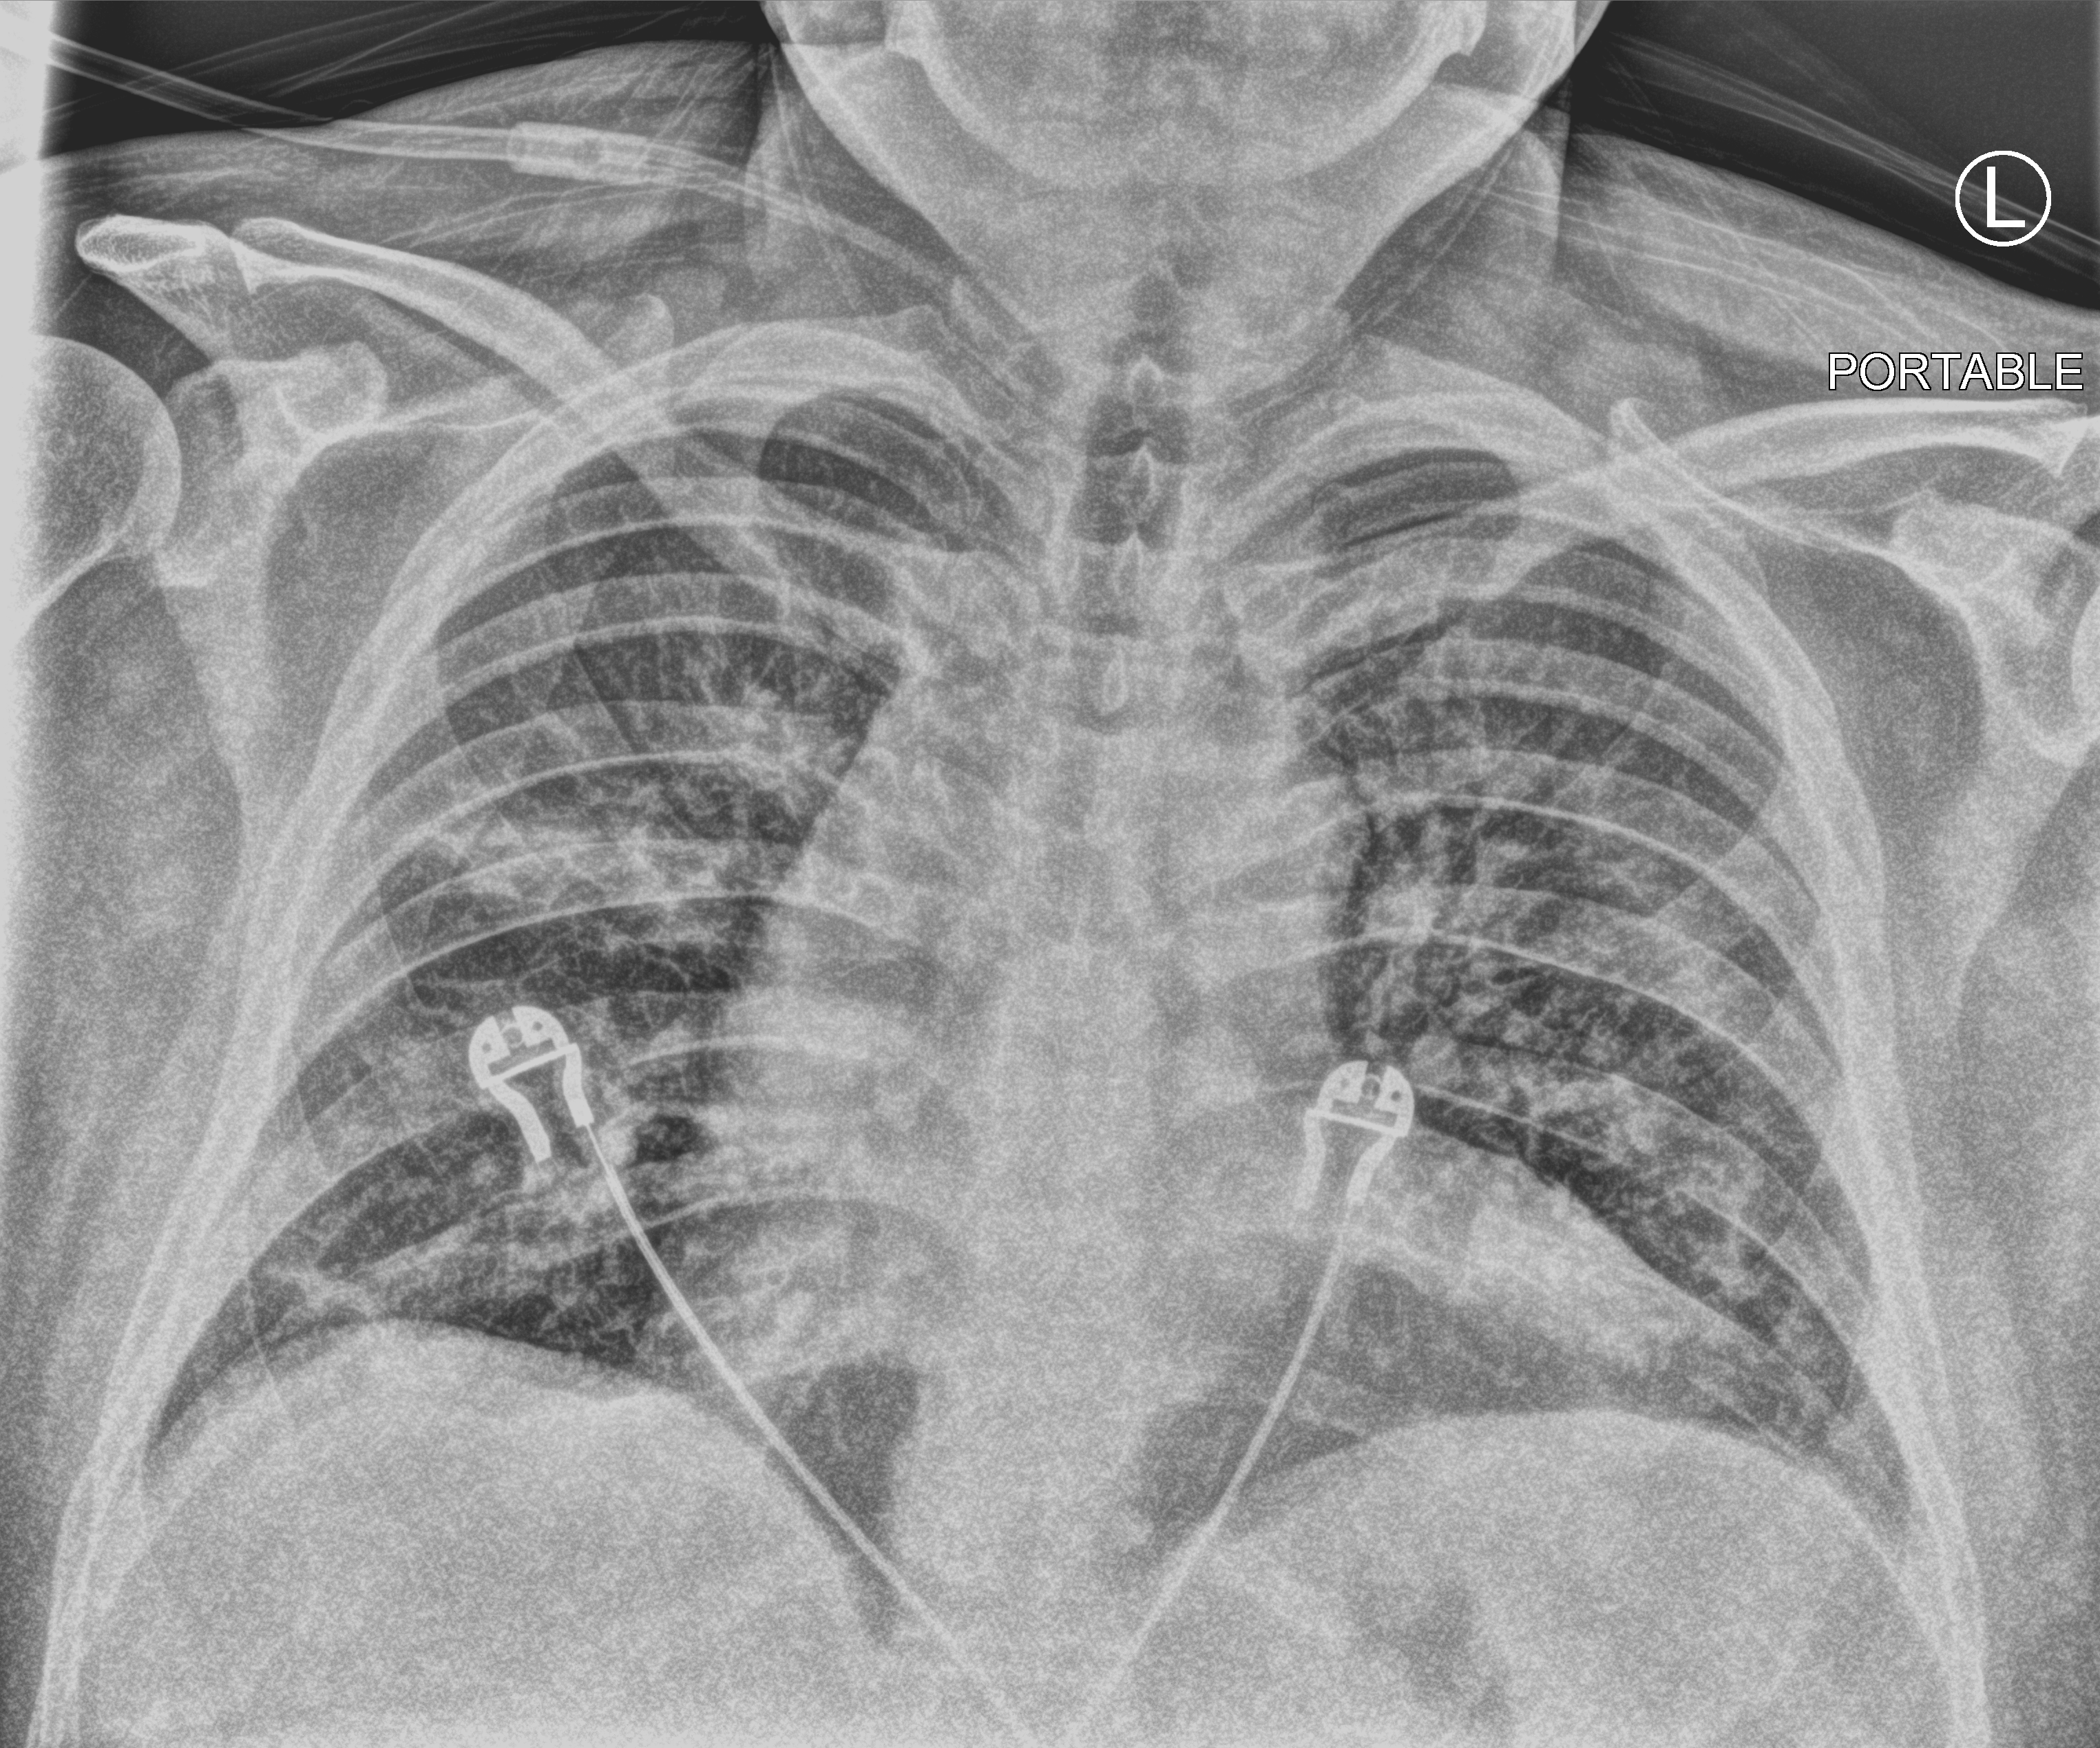
Portable chest radiograph; anteroposterior (AP) projection. Patient hospitalised with COVID-19; male, aged 18–59 years.
Admission-level facts for this patient (not findings on this image; timing relative to this image not recorded): admitted to intensive care during this hospital stay: no; smoking status (admission record): current; mechanically ventilated during this hospital stay: no.